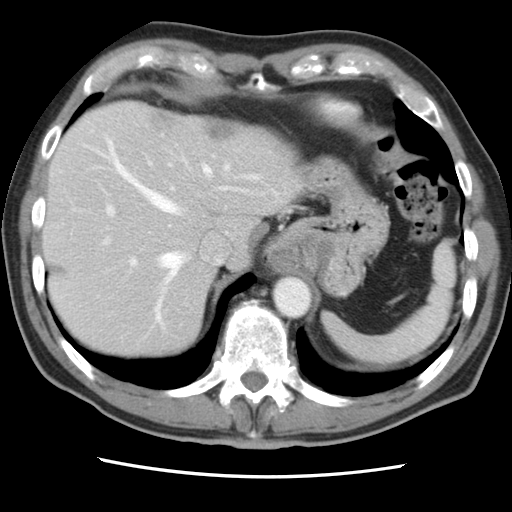
Contrast-enhanced abdominal CT, one axial slice; slice 66 of 83 in the series (ordered by position); 120 kVp; intravenous contrast given; soft-tissue window (W 400 / L 40 HU); 512 × 512 image matrix. Male patient, age 69 years. Case-level facts recorded for this patient, not image findings: diagnosis: colorectal cancer liver metastases, imaged before liver resection; multiple liver metastases: yes; largest metastasis: 3.5 cm.
Structures marked on this image (manually delineated by an expert):
- hepatic veins: box from (x=83, y=136) to (x=257, y=322) px
- liver: (x=44, y=101)–(x=295, y=356)
- planned liver remnant (the part of the liver to remain after resection): (x=44, y=146)–(x=215, y=356)
- portal vein (with intrahepatic branches): (x=104, y=161)–(x=174, y=266)
- liver metastasis: (x=156, y=114)–(x=176, y=127)
- liver metastasis: (x=207, y=124)–(x=232, y=135)